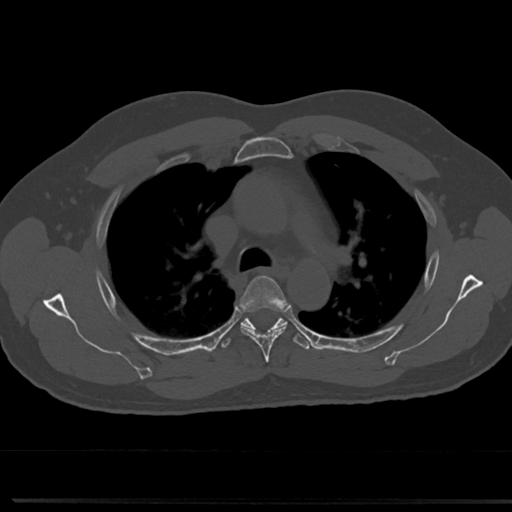
CT including the spine, one axial slice. Position 528 of 817 along the scan axis. Reconstruction kernel Br40s/3. 120 kVp. Bone window (W 1800 / L 400 HU). 512 × 512 image matrix, field of view 355 × 355 mm. Male patient, age 61 years. From the clinical record (not read from this slice): primary cancer: prostate.
Annotated regions visible in this slice (semi-automatically segmented with operator editing):
- T4 vertebra: bounding box (x1, y1, x2, y2) in pixels: (238, 276, 289, 358)
- T5 vertebra: (242, 320, 285, 329)